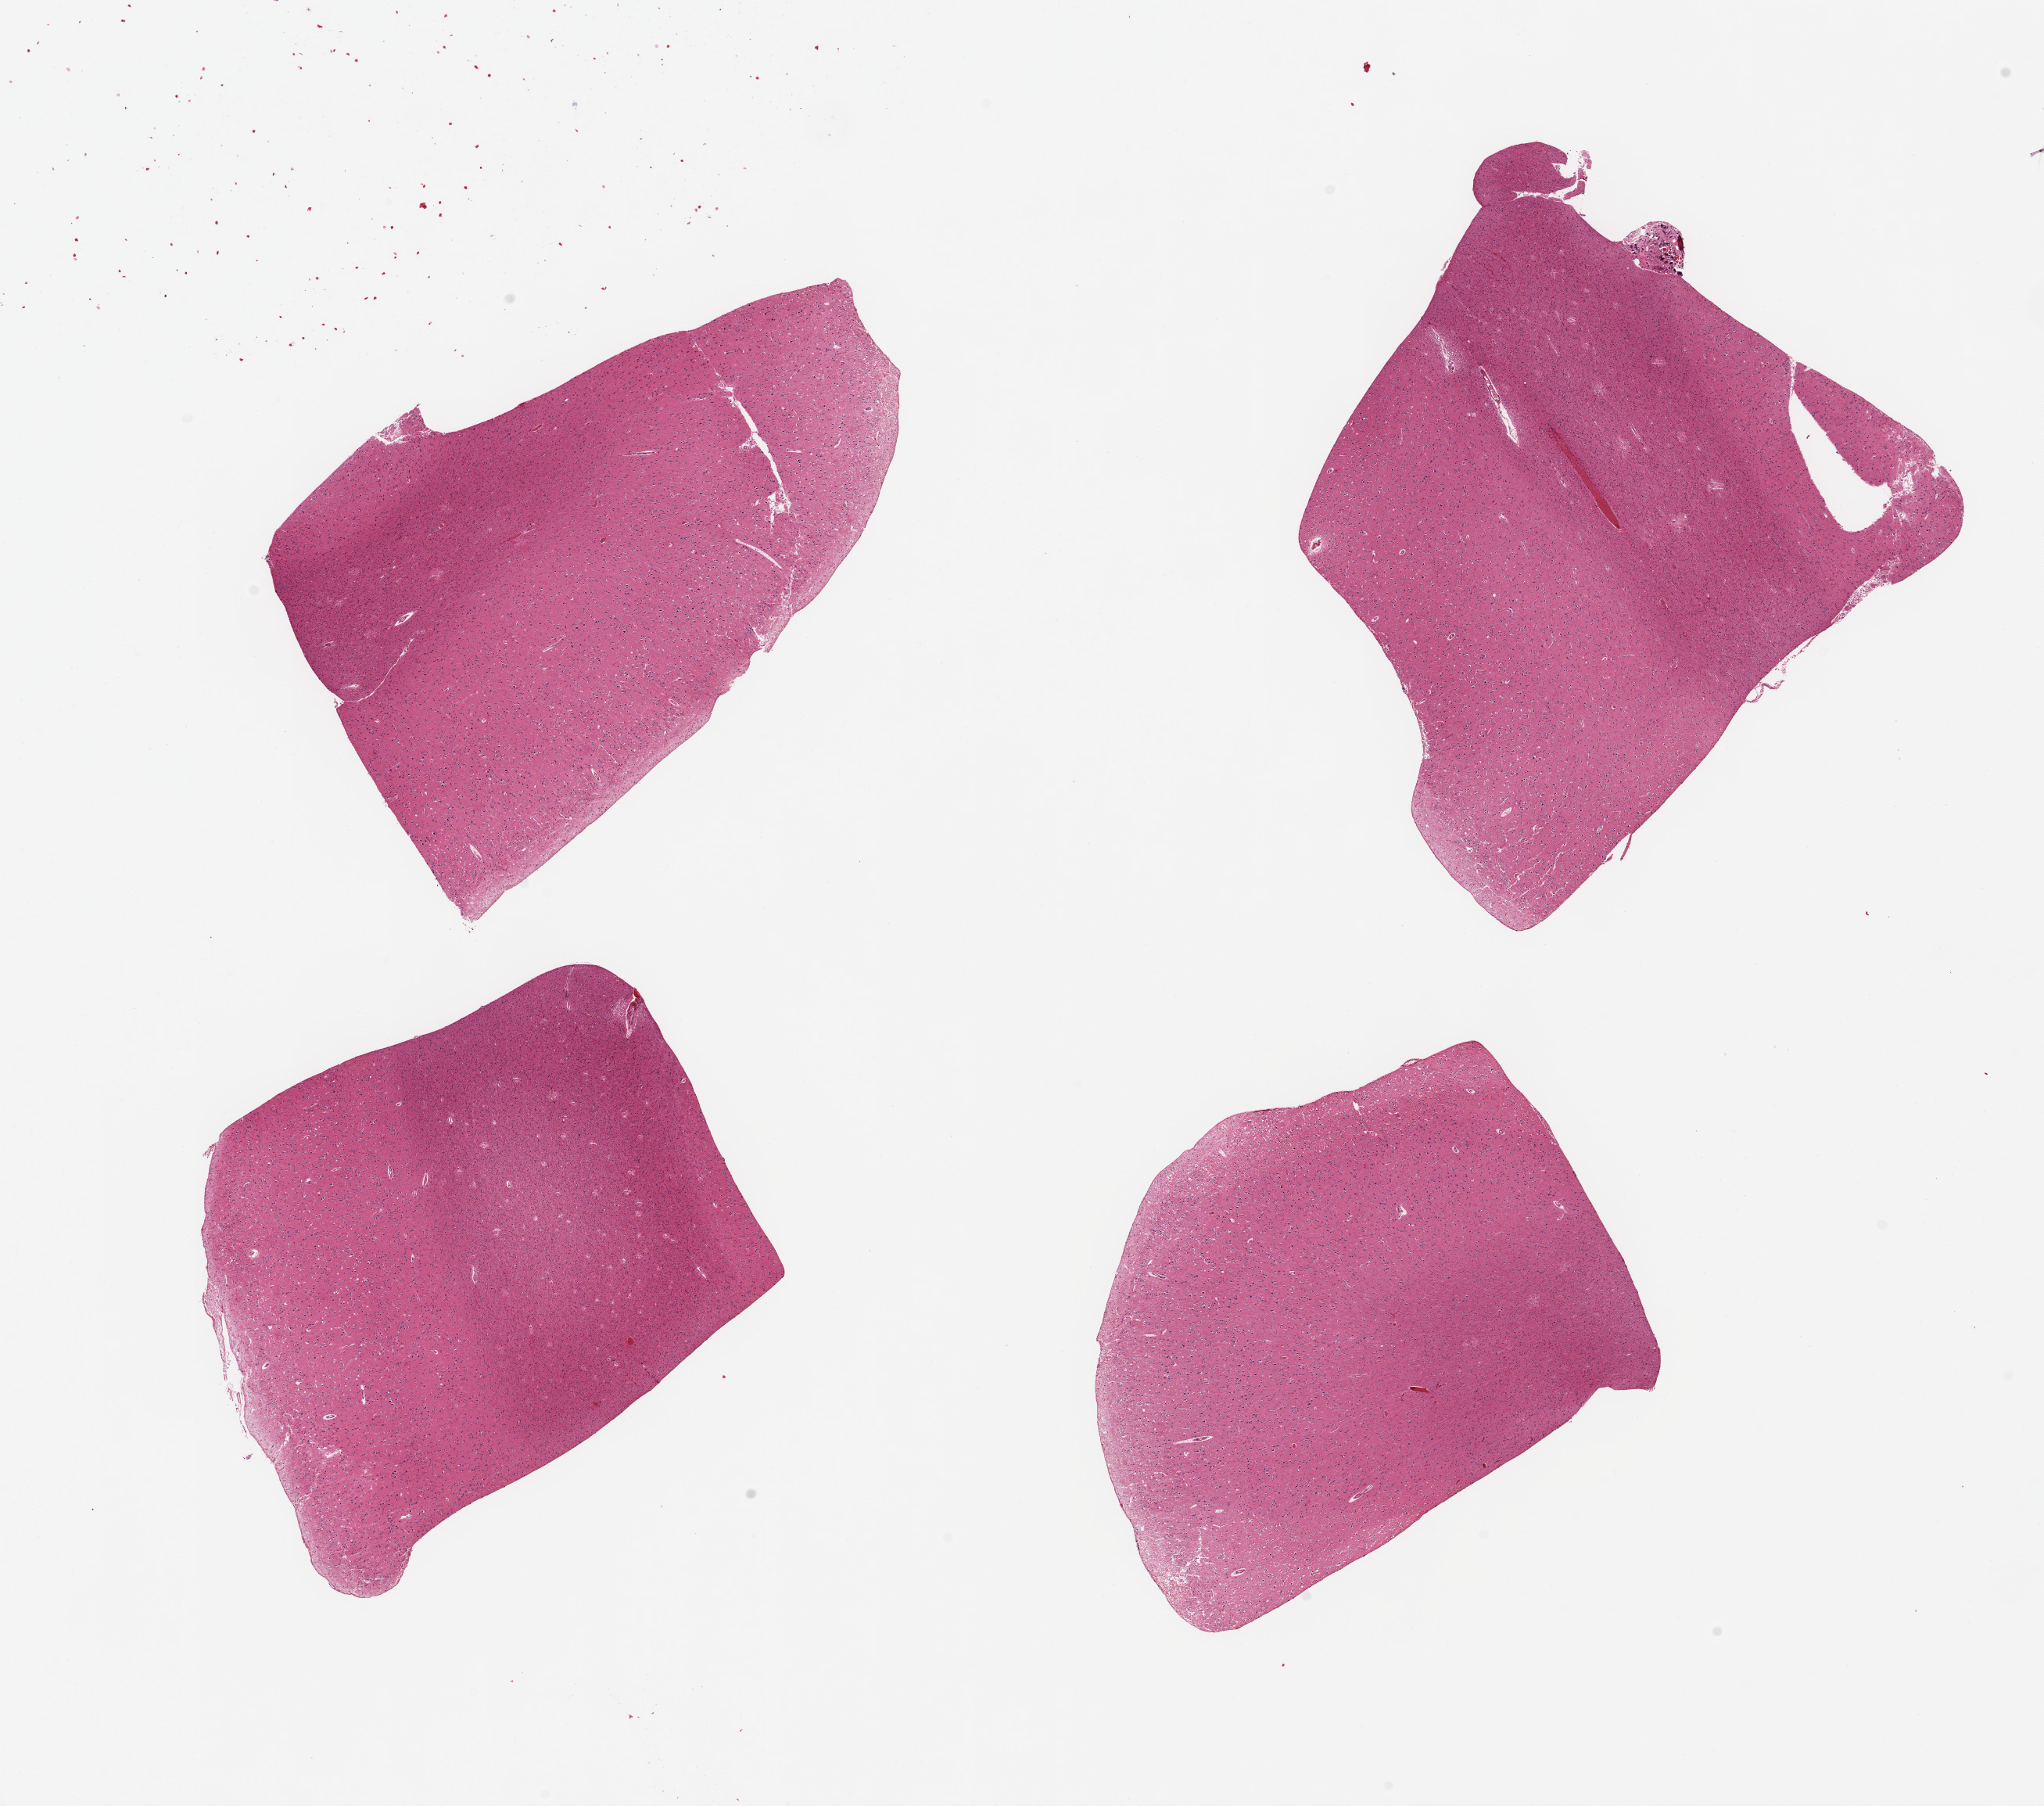
H&E whole-slide image, low-resolution overview of the scanned area, about 20.7 x 18.3 mm. PAXgene-fixed paraffin-embedded (PFPE) section. Target tissue: cerebral cortex. Donor tissue sample.
Review note (as recorded): 4 pieces, no abnormalities.